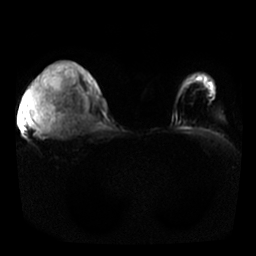
Breast MRI, one axial slice; slice 20 of 25 in the series (ordered by position); diffusion-weighted series; image 2 of 4 stored at this slice position (different b-values; order by instance number); 1.5 T; 256 × 256 image matrix. Female patient.
Annotated regions visible in this slice (outlined manually by an expert reader):
- tumour on diffusion-weighted imaging: bounding box [x1, y1, x2, y2] px = [25, 75, 92, 133]